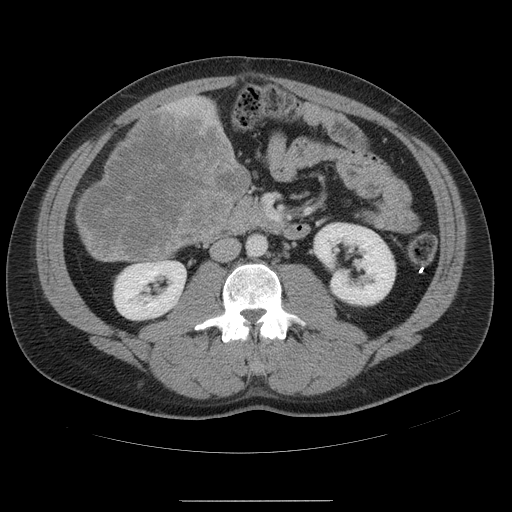
Contrast-enhanced abdominal CT, one axial slice; slice 15 of 54 in the series (ordered by position); 120 kVp; intravenous contrast given; soft-tissue window (W 400 / L 40 HU); 5 mm slice thickness; 512 × 512 image matrix, field of view 436 × 436 mm. Male patient, age 40 years. Case-level facts recorded for this patient, not image findings: diagnosis: colorectal cancer liver metastases, imaged before liver resection; multiple liver metastases: no; largest metastasis: 15 cm.
Structures marked on this image (expert manual segmentation):
- liver: bounding box <76,97,250,264> (left, top, right, bottom; pixels)
- liver metastasis: <76,110,250,261>